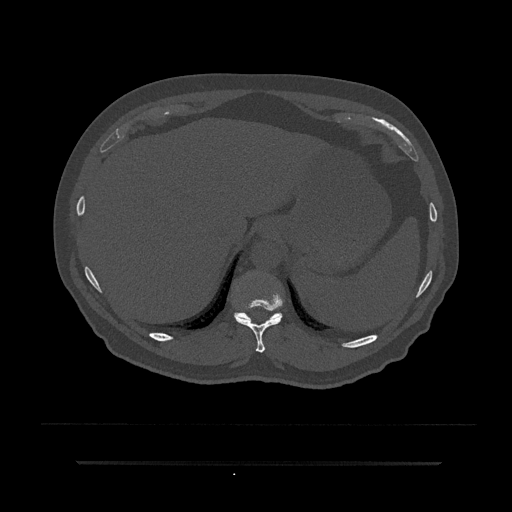
CT including the spine, one axial slice; slice 306 of 797 in the series (ordered by position); reconstruction kernel Br40s/3; bone window (W 1800 / L 400 HU); 0.5 mm slice thickness; 512 × 512 image matrix, field of view 464 × 464 mm. Male patient, age 59 years. Case-level facts recorded for this patient, not image findings: primary cancer: bile ducts; vertebrae with lytic lesions (as recorded): T10.
Annotated regions visible in this slice (semi-automatically segmented with operator editing):
- T10 vertebra: bounding box <234,292,284,353> (left, top, right, bottom; pixels)
- T11 vertebra: <234,312,282,323>